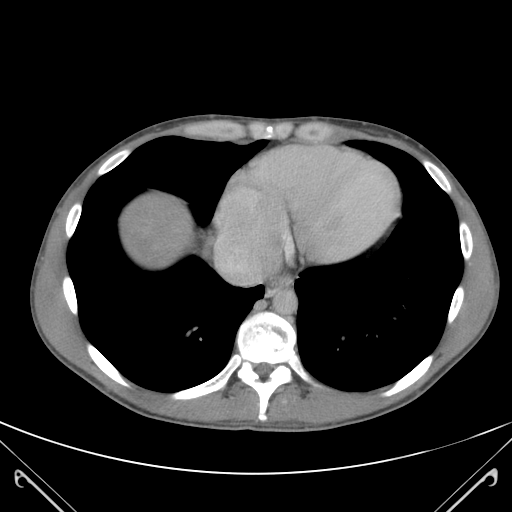
Contrast-enhanced abdominal CT (liver protocol), one axial slice. Position 110 of 118 along the scan axis. Soft-tissue window (W 400 / L 40 HU). 3 mm slice thickness. 512 × 512 image matrix, field of view 380 × 380 mm. From the clinical record (not read from this slice): diagnosis: hepatocellular carcinoma (patient treated with transarterial chemoembolisation; whether this scan precedes or follows treatment is not stated here); TNM stage (as recorded): Stage-IIIB; Child-Pugh class: A.
Outlined on this slice (semi-automatically segmented with operator editing):
- abdominal aorta: bounding box [x1, y1, x2, y2] px = [273, 291, 298, 314]